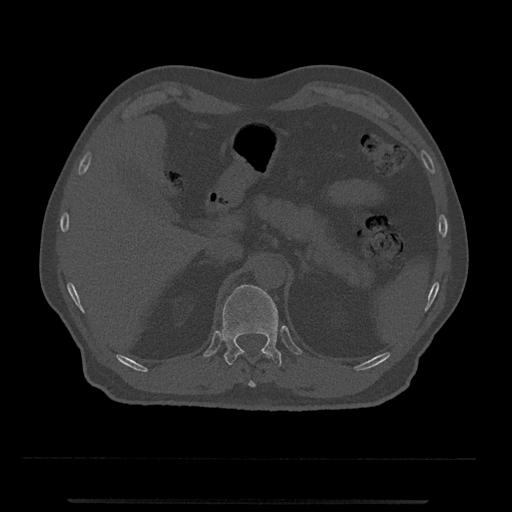
CT including the spine, one axial slice. Slice 419 of 797 in the series (ordered by position). Reconstruction kernel Br40s/3. Bone window (W 1800 / L 400 HU). 512 × 512 image matrix, field of view 419 × 419 mm. Male patient, age 63 years. Case-level facts recorded for this patient, not image findings: primary cancer: prostate.
Structures marked on this image (semi-automatic segmentation, software-assisted and operator-edited):
- T11 vertebra: bounding box (x1, y1, x2, y2) in pixels: (236, 351, 271, 387)
- T12 vertebra: (222, 285, 282, 366)